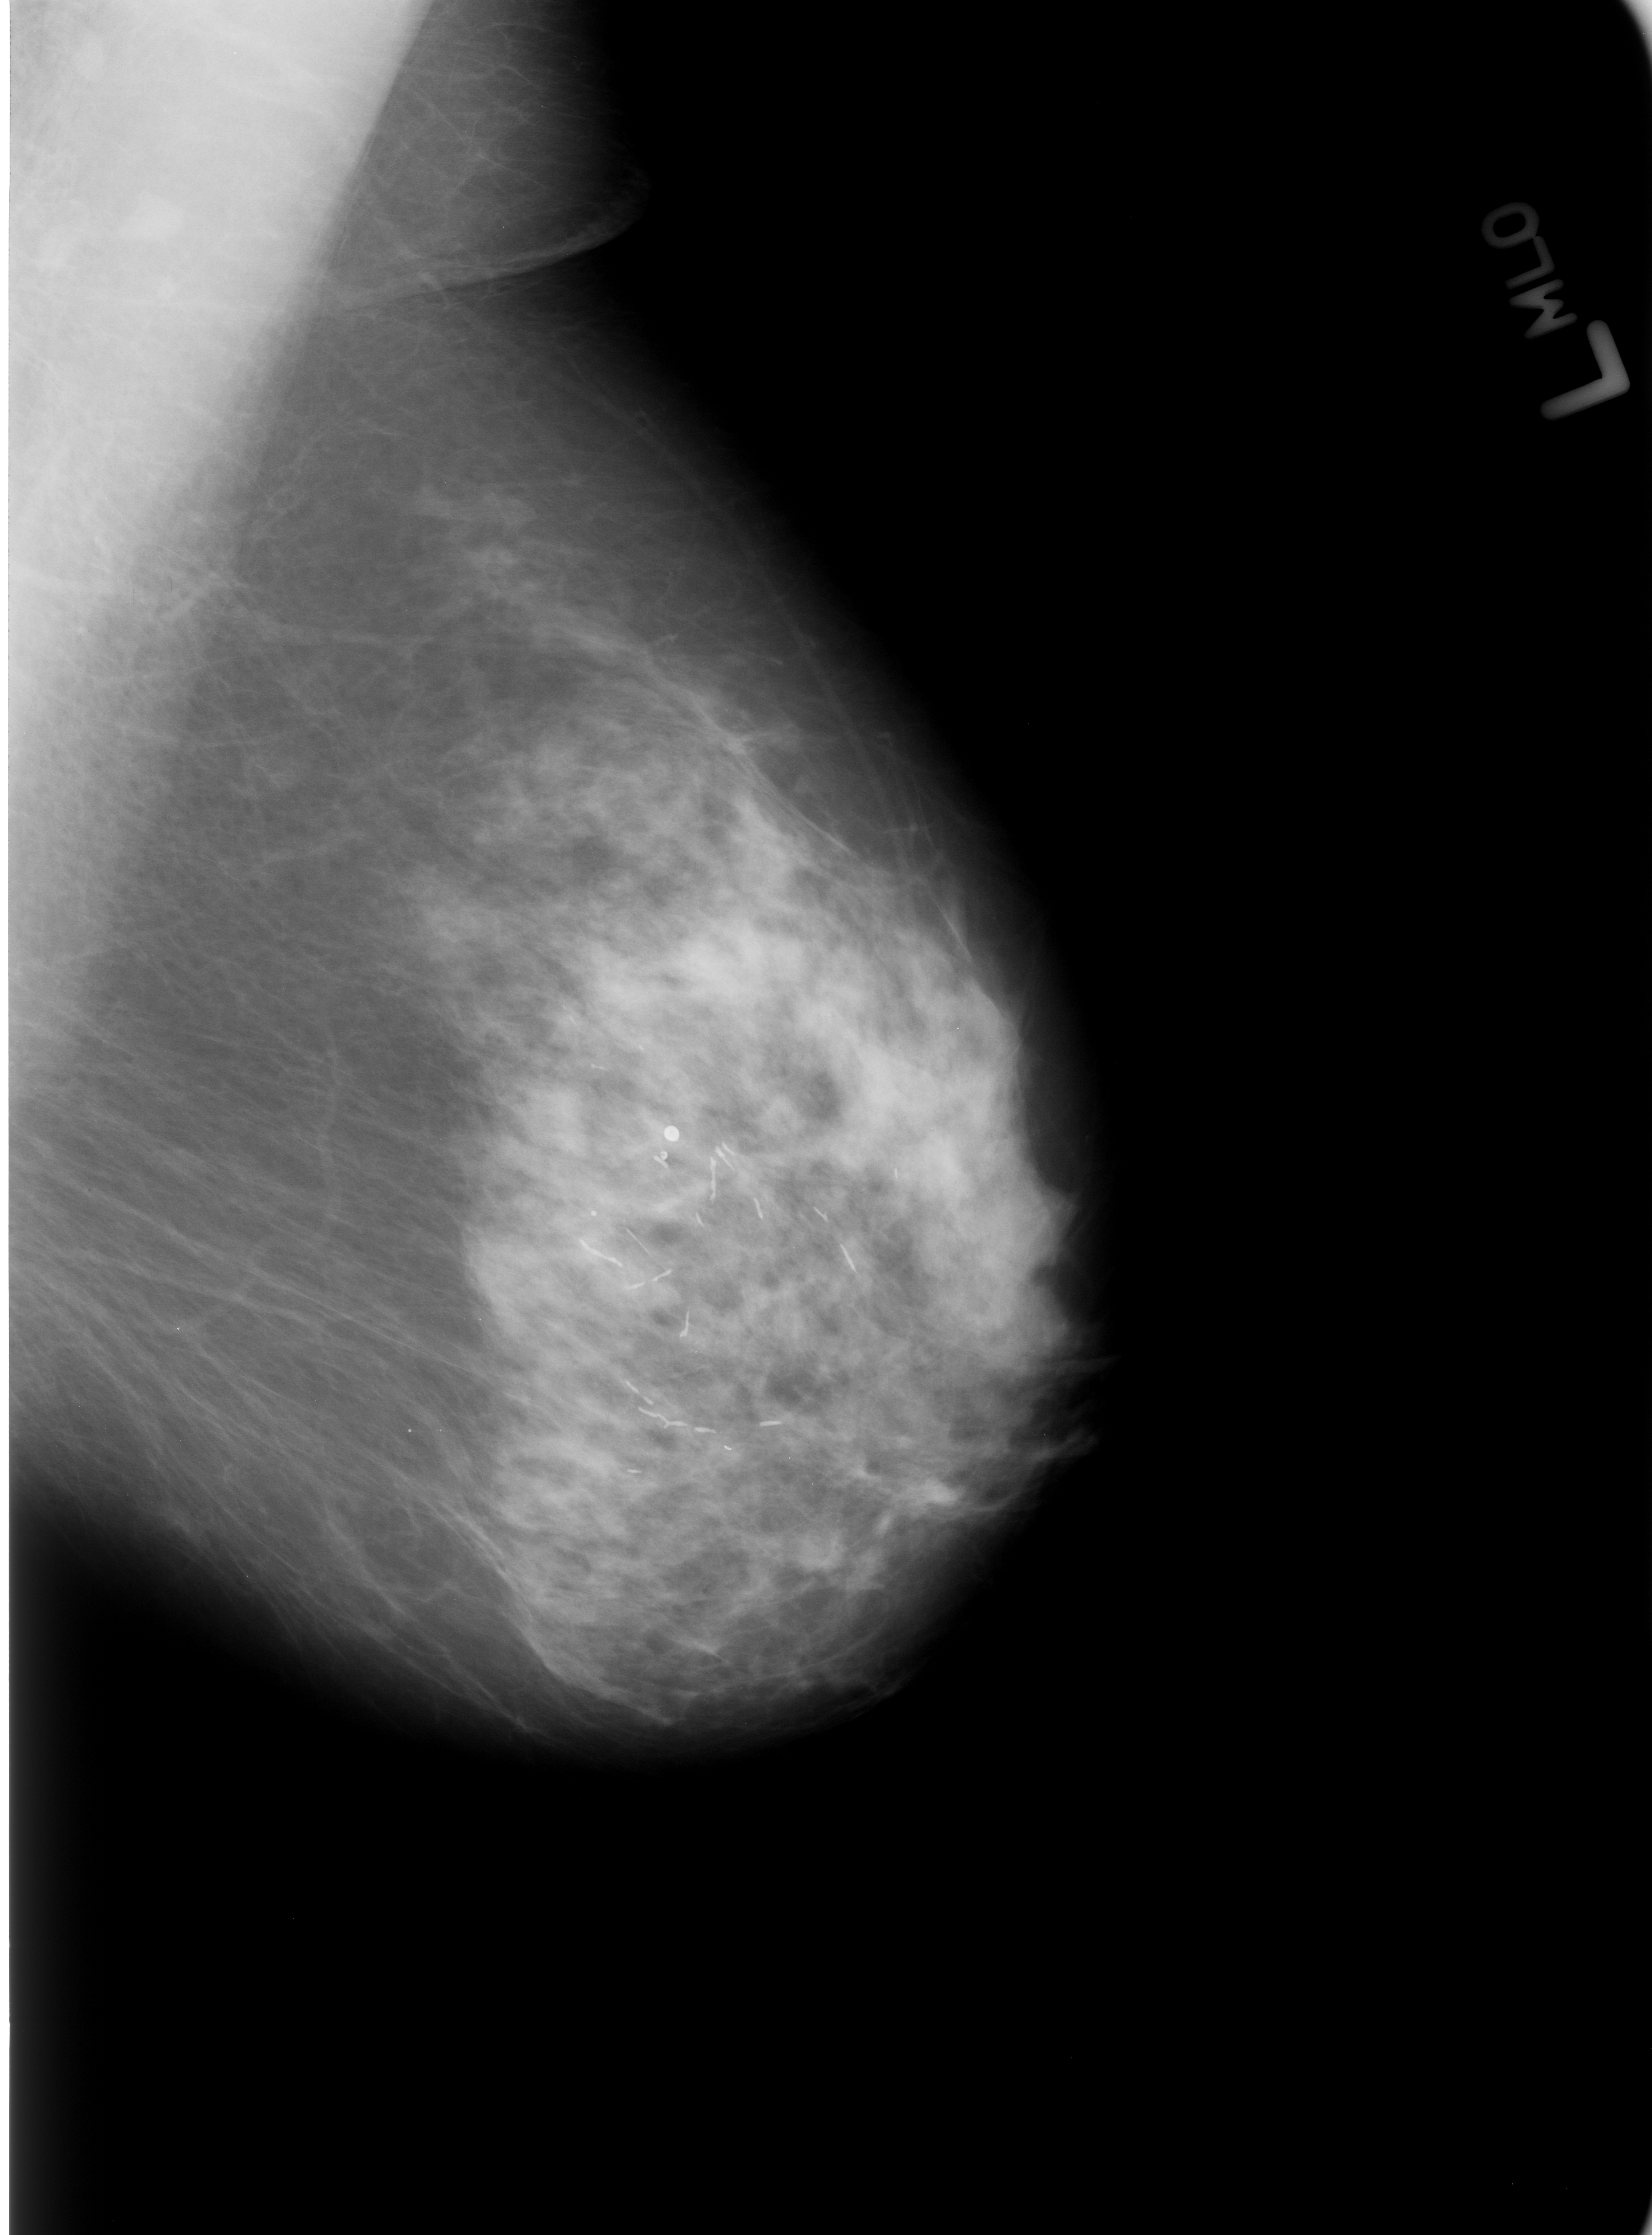
Mammogram (digitized film). Left breast. Mediolateral oblique (MLO) view. BI-RADS breast density category 3 (scale 1–4). 1652 × 2235 image matrix.
Marked abnormalities (boxes around the expert regions of interest):
- Finding 1 of 5: calcifications, morphology large rodlike / round and regular, distribution regional; BI-RADS assessment category 2; subtlety rating 5 on a 1 (subtle) to 5 (obvious) scale; outcome (as recorded, no biopsy): benign without callback (not worked up further): bounding box (x1, y1, x2, y2) in pixels: (576, 1229, 689, 1298)
- Finding 2 of 5: calcifications, morphology large rodlike / round and regular, distribution regional; BI-RADS assessment category 2; subtlety rating 5 on a 1 (subtle) to 5 (obvious) scale; benign; no additional work-up was recommended (outcome (as recorded, no biopsy): benign without callback): (617, 1367, 808, 1439)
- Finding 3 of 5: calcifications, morphology large rodlike / round and regular, distribution regional; BI-RADS assessment category 2; subtlety rating 5 on a 1 (subtle) to 5 (obvious) scale; outcome (as recorded, no biopsy): benign without callback (not worked up further): (646, 1120, 689, 1173)
- Finding 4 of 5: calcifications, morphology large rodlike / round and regular, distribution regional; BI-RADS assessment category 2; outcome (as recorded, no biopsy): benign without callback (not worked up further): (707, 1139, 782, 1230)
- Finding 5 of 5: calcifications, morphology large rodlike / round and regular, distribution regional; BI-RADS assessment category 2; subtlety rating 5 on a 1 (subtle) to 5 (obvious) scale; benign; no additional work-up was recommended (outcome (as recorded, no biopsy): benign without callback): (813, 1200, 872, 1288)